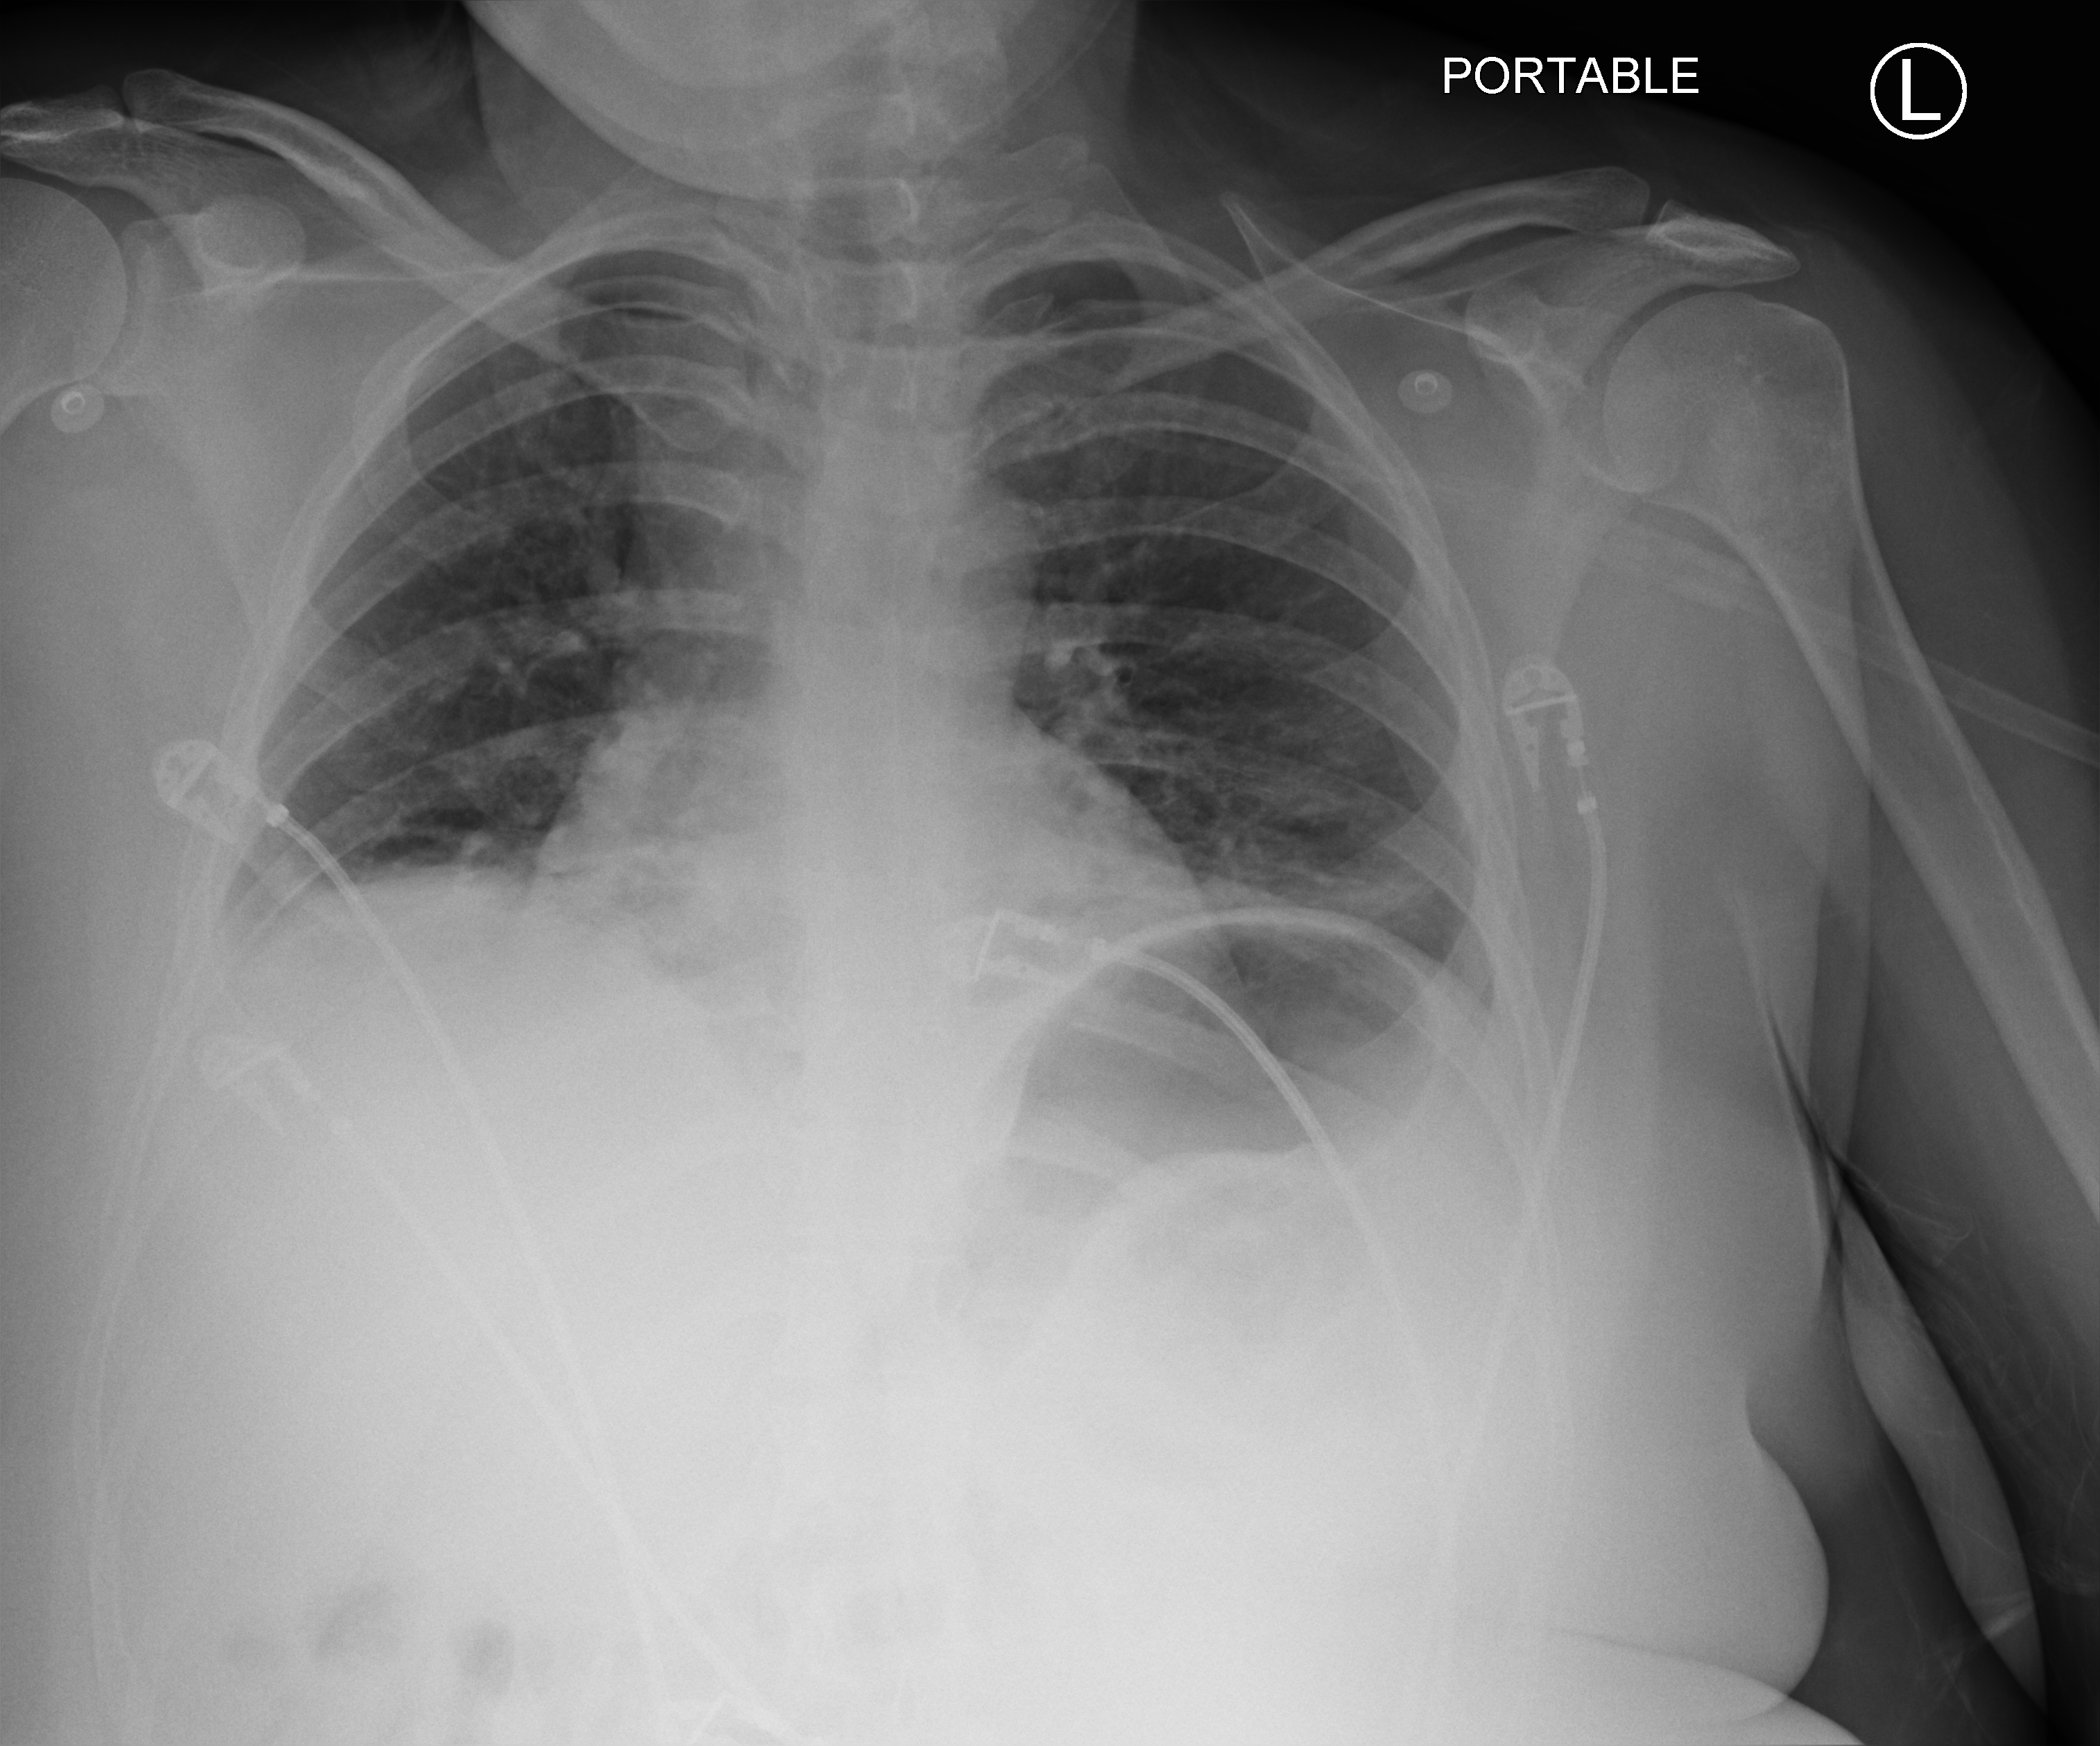
Chest X-ray (portable); anteroposterior (AP) projection. Female patient hospitalised with COVID-19, age 18–59 years.
Hospital-stay facts (about this admission, not read from this image; timing relative to this image not recorded): other chronic lung disease (admission record): no; admitted to intensive care during this hospital stay: no.